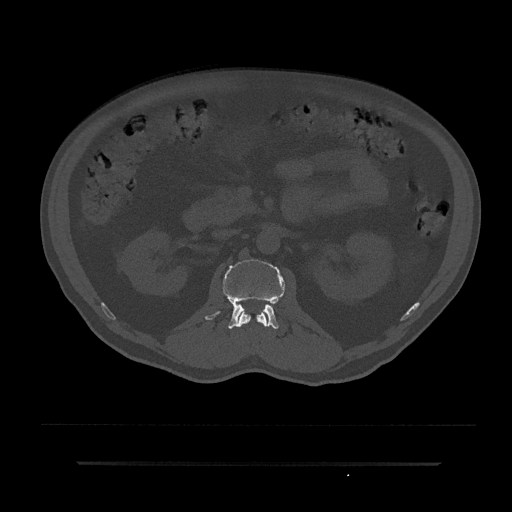
CT including the spine, one axial slice. Position 101 of 797 along the scan axis. 120 kVp. Bone window (W 1800 / L 400 HU). 512 × 512 image matrix, field of view 464 × 464 mm. Male patient, age 59 years. Case-level facts recorded for this patient, not image findings: primary cancer: bile ducts.
Structures marked on this image (semi-automatic segmentation, software-assisted and operator-edited):
- L1 vertebra: bounding box <237,311,268,327> (left, top, right, bottom; pixels)
- L2 vertebra: <205,259,285,329>